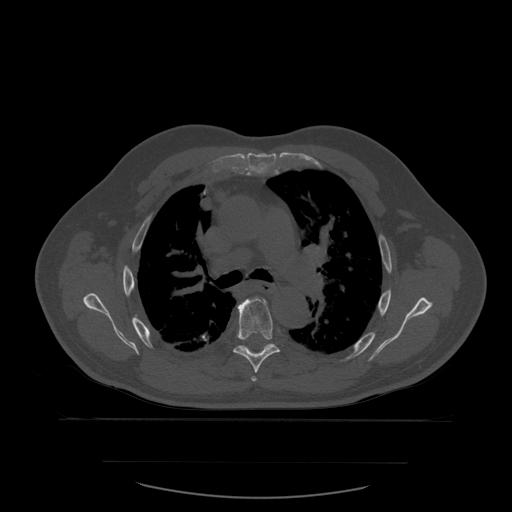
CT including the spine, one axial slice. Slice 404 of 590 in the series (ordered by position). Bone window (W 1800 / L 400 HU). 1.25 mm slice thickness. 512 × 512 image matrix. Patient age 71 years. From the clinical record (not read from this slice): primary cancer: lung; vertebrae with lytic lesions (as recorded): T1, T2, L5, S1.
Outlined on this slice (semi-automatic segmentation, software-assisted and operator-edited):
- T5 vertebra: bounding box (x1, y1, x2, y2) in pixels: (252, 377, 257, 382)
- T6 vertebra: (233, 298, 280, 374)
- T7 vertebra: (238, 344, 275, 353)